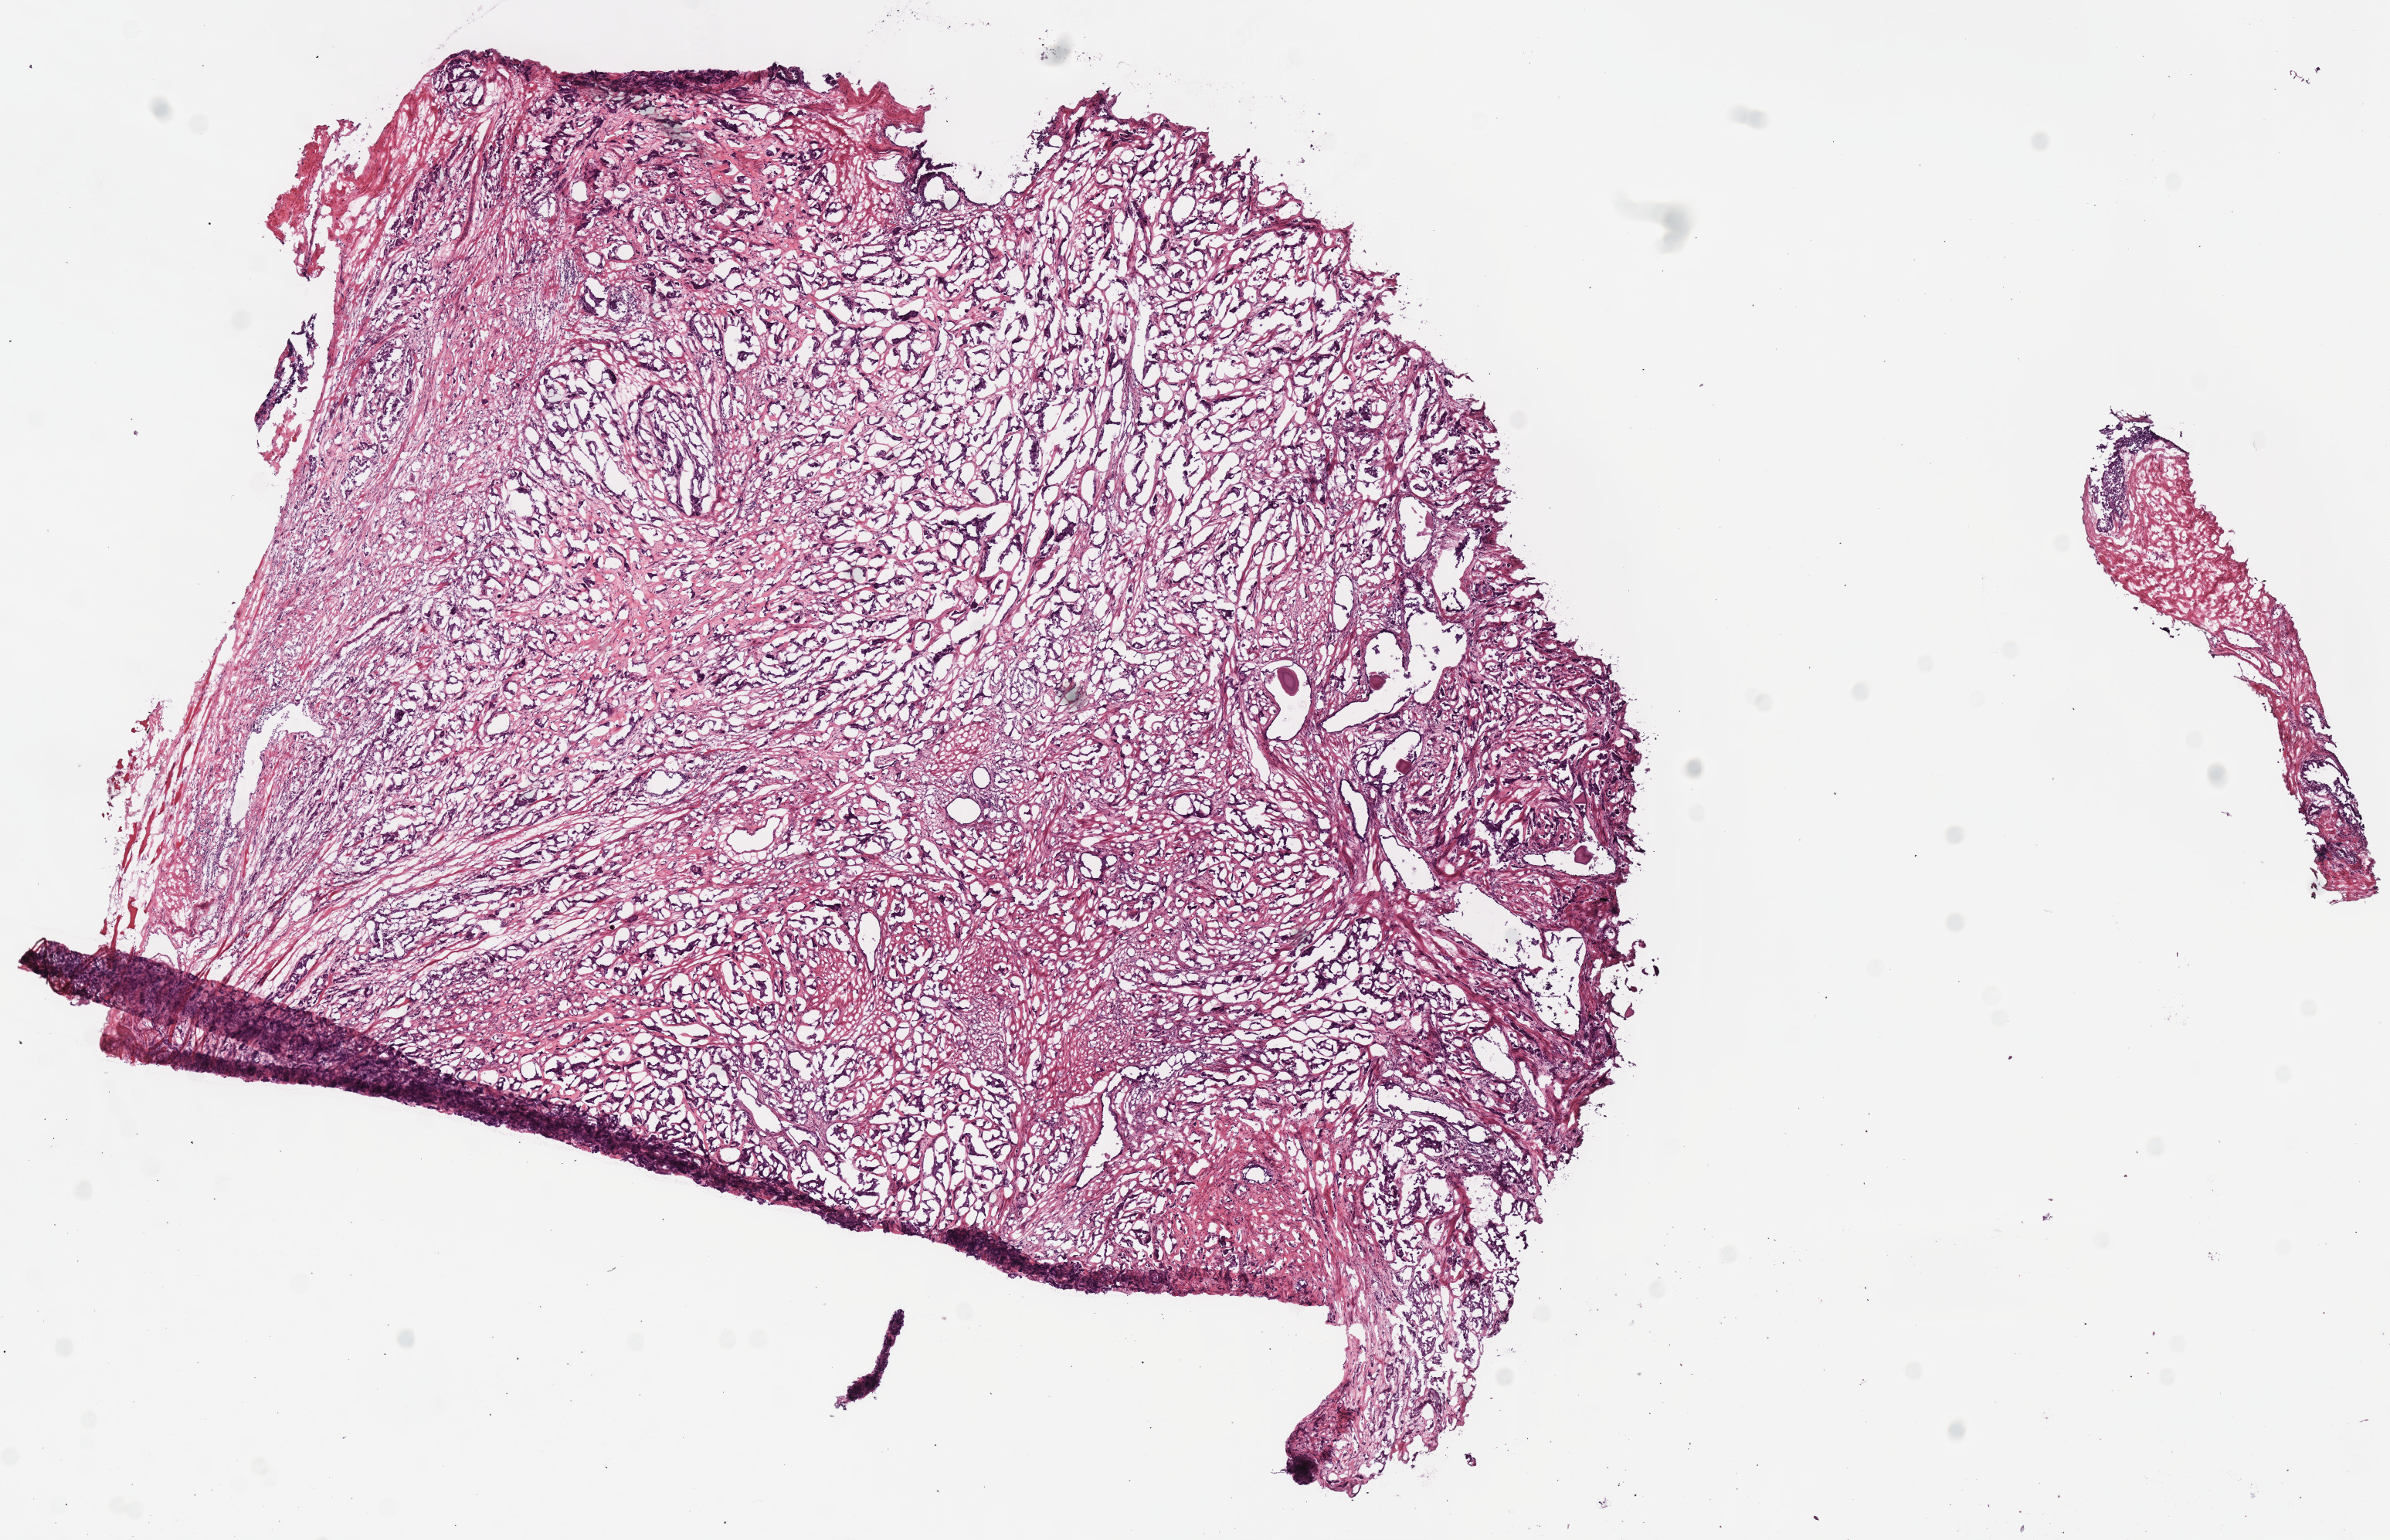
H&E-stained whole-slide image, a low-resolution overview of the entire scanned area, about 12.2 x 7.9 mm; frozen section from the top of the tissue portion; sample: primary tumour, prostate. Male patient; age at initial diagnosis 52 years. Gleason score: 8 (4+4). Pathologist review of this section (percent, as recorded): tumour cells 80%, tumour nuclei 80%, normal cells 5%, stromal cells 15%, necrosis 0%.
Laterality: bilateral. Pathologic diagnosis: Acinar cell carcinoma.